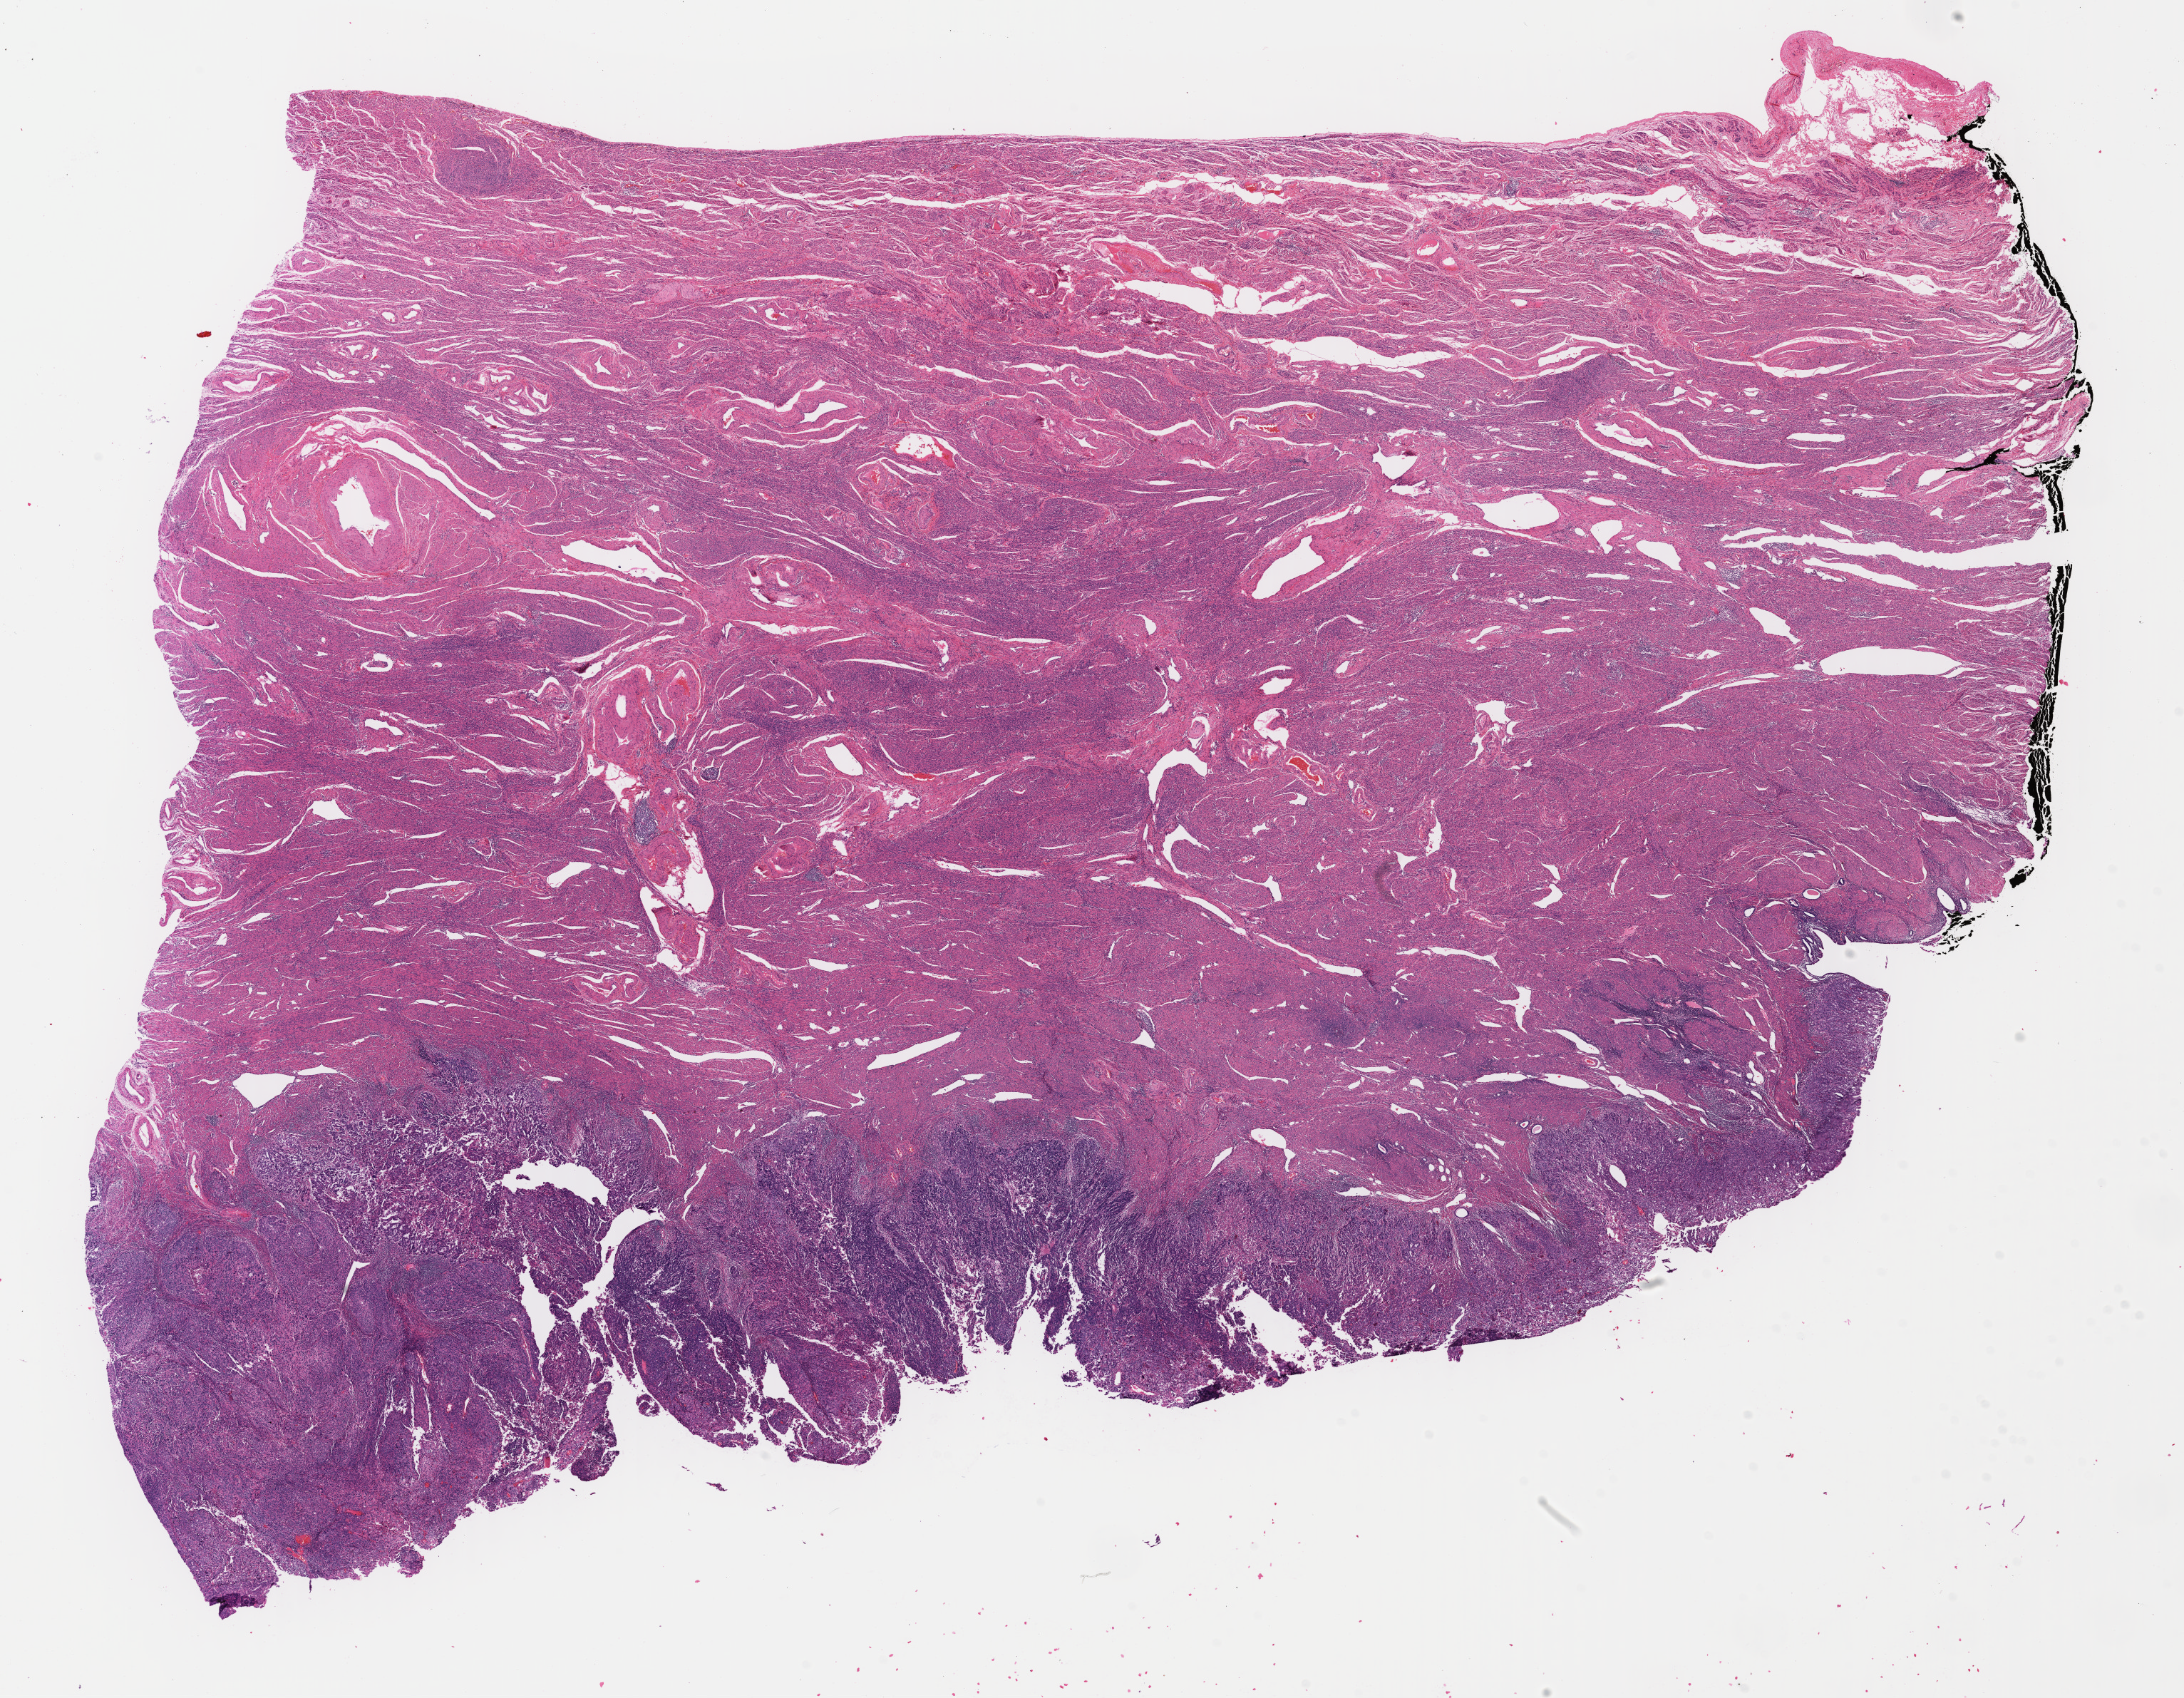
Digitized H&E-stained tissue section (whole slide), shown as a low-resolution overview of the whole scanned area (about 24.1 x 18.7 mm, slide scanned at 40x). Formalin-fixed paraffin-embedded (FFPE) diagnostic section. Uterus, primary tumour sample. Female, age 65 years at initial diagnosis. Histologic grade: G3 (poorly differentiated).
• histologic diagnosis: Endometrioid adenocarcinoma, NOS (endometrium)
• FIGO stage: IIIA